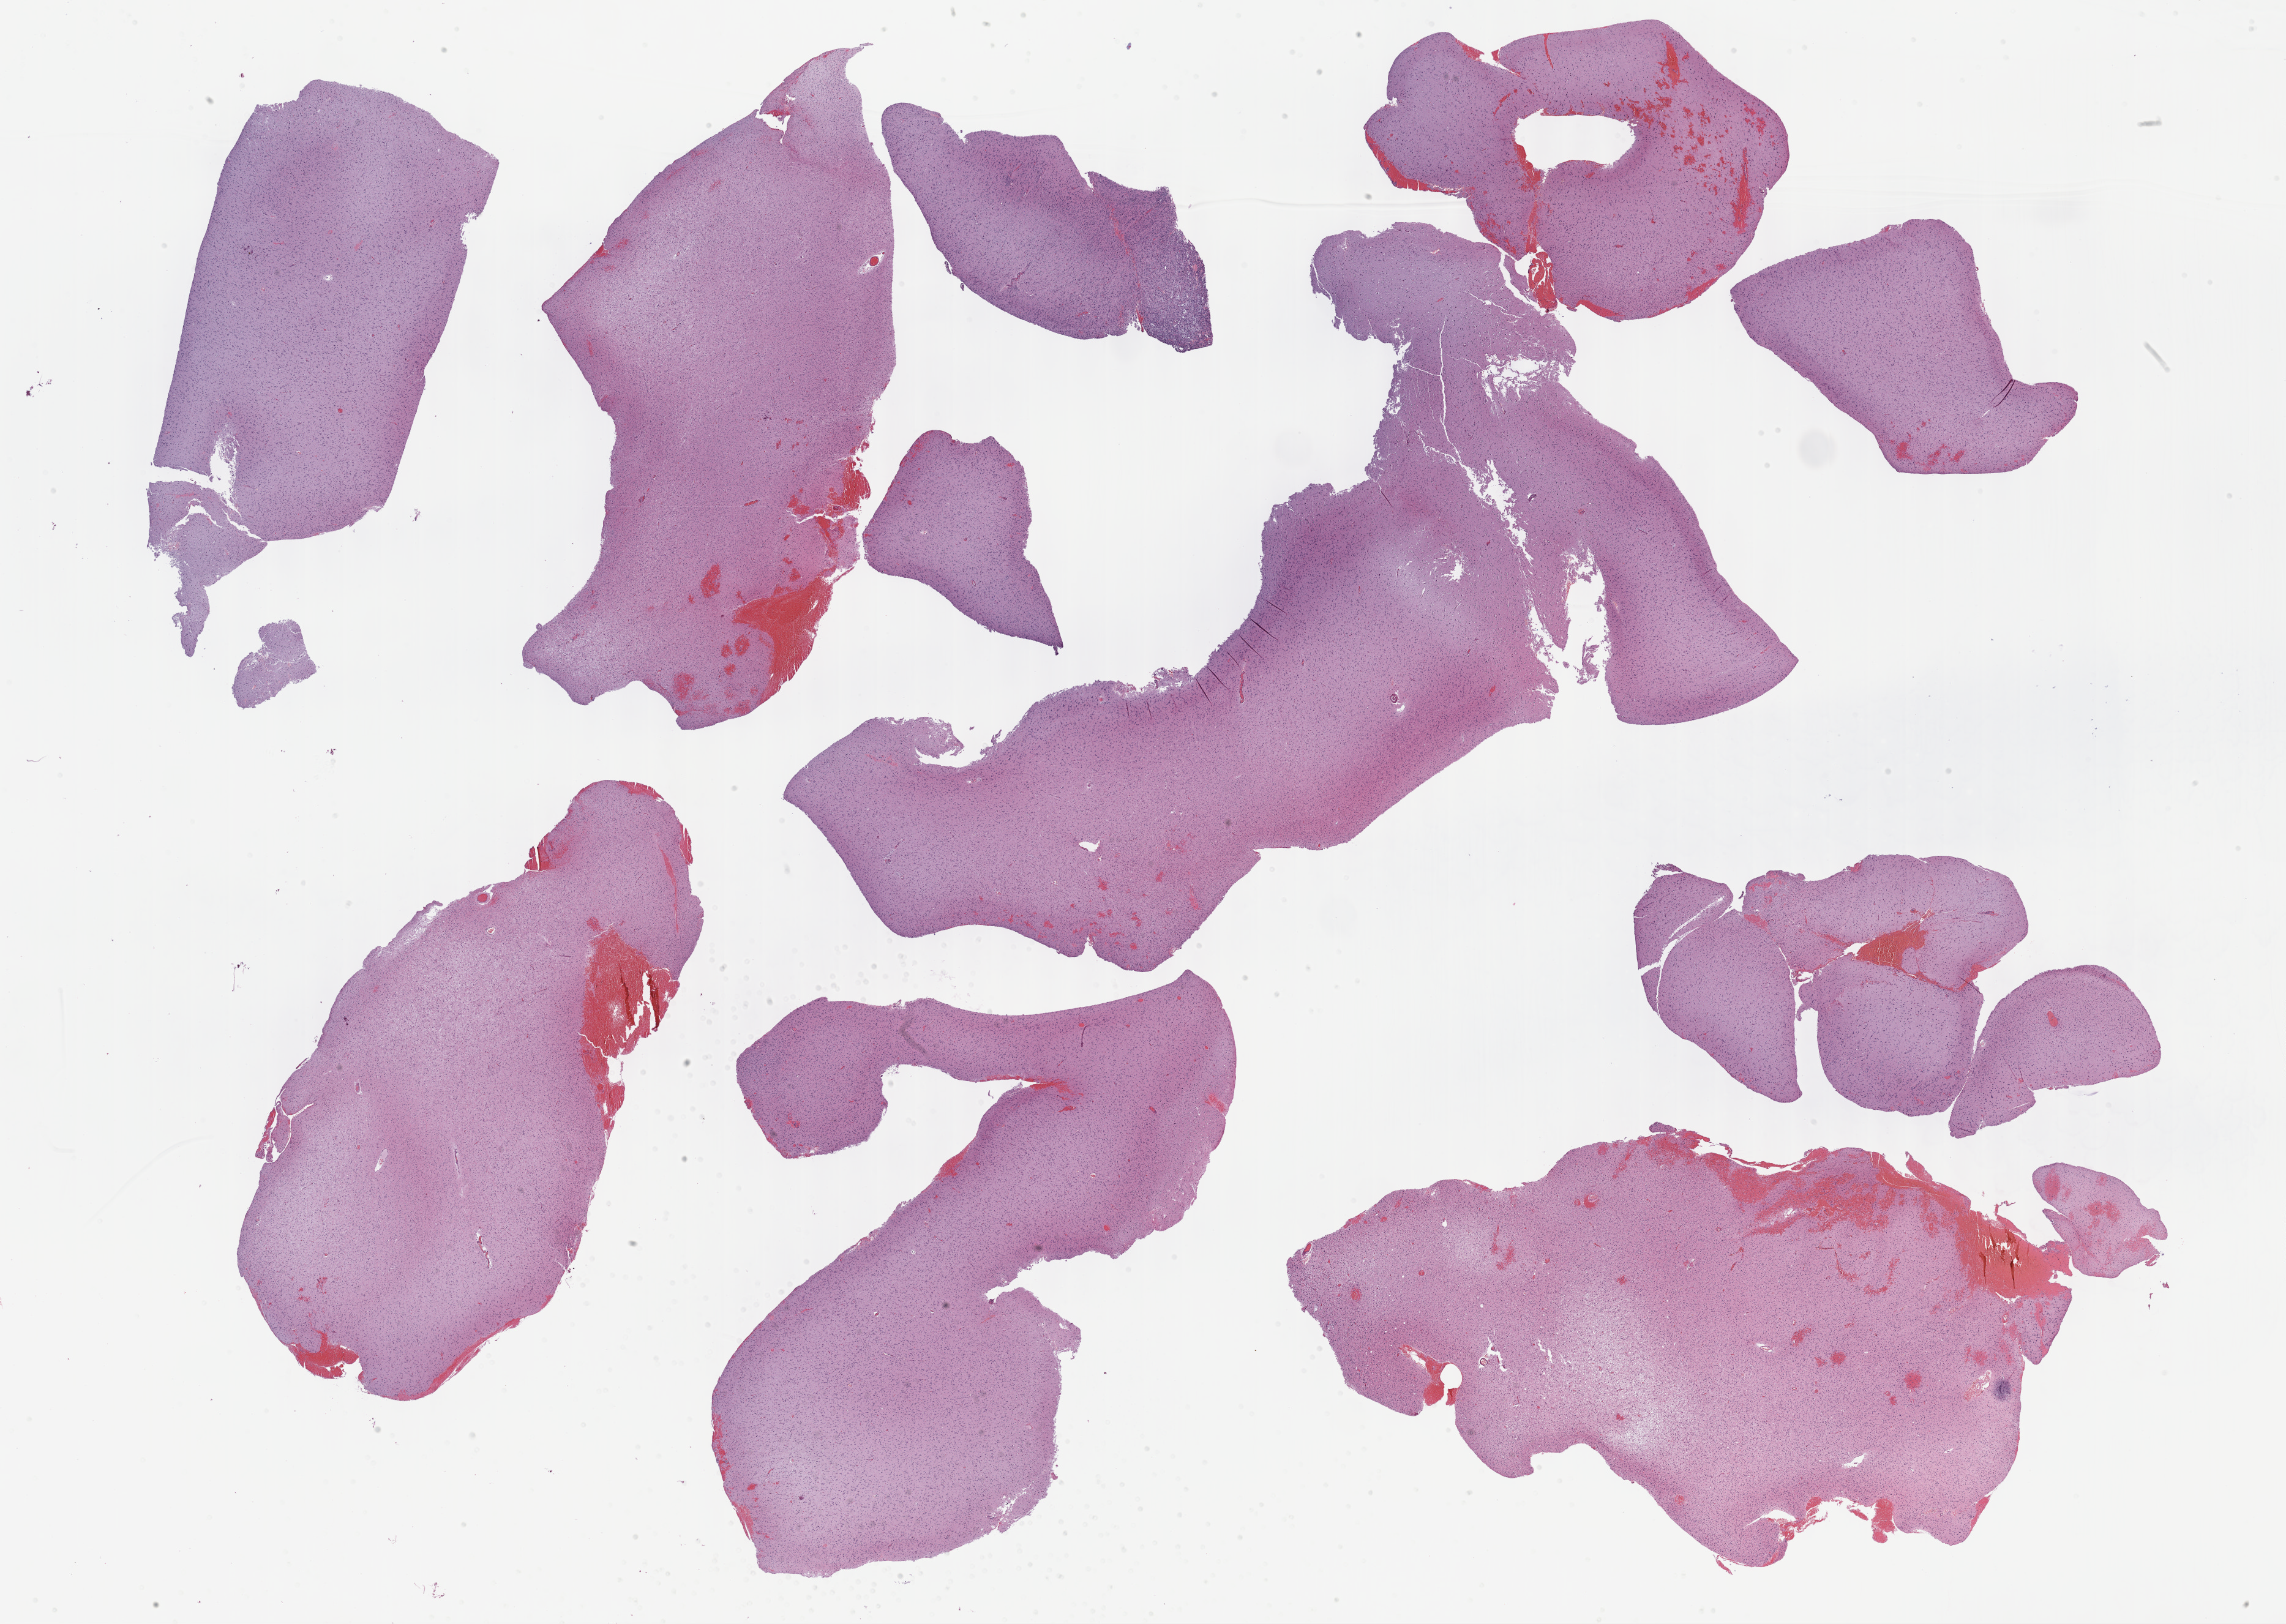
Whole-slide histology image, H&E-stained, shown as a low-resolution overview of the whole scanned area (about 30.2 x 21.5 mm, slide scanned at 40x), formalin-fixed paraffin-embedded (FFPE) diagnostic section, sample: primary tumour, brain. Patient: male, age at initial diagnosis 54 years. Histologic grade: G2 (moderately differentiated).
* laterality: left
* histologic diagnosis: Oligodendroglioma, NOS (cerebrum)